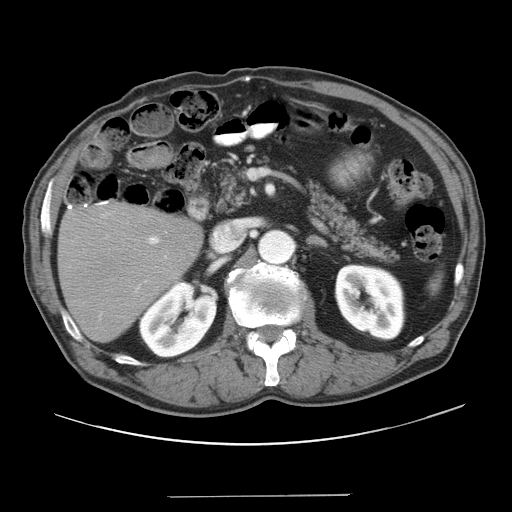
Contrast-enhanced abdominal CT, one axial slice. Position 18 of 41 along the scan axis. Intravenous contrast given. Soft-tissue window (W 400 / L 40 HU). 5 mm slice thickness. 512 × 512 image matrix, field of view 420 × 420 mm. Male patient, age 75 years. From the clinical record (not read from this slice): diagnosis: colorectal cancer liver metastases, imaged before liver resection; multiple liver metastases: no; largest metastasis: 5.2 cm; disease in both lobes: no.
Structures marked on this image (manually delineated by an expert):
- liver: box from (x=60, y=204) to (x=200, y=342) px
- planned liver remnant (the part of the liver to remain after resection): (x=60, y=205)–(x=200, y=341)
- portal vein (with intrahepatic branches): (x=100, y=236)–(x=167, y=315)